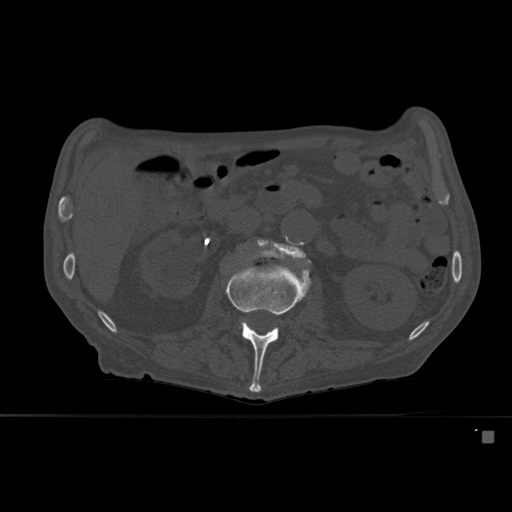
CT including the spine, one axial slice; bone window (W 1800 / L 400 HU); 1.5 mm slice thickness; 512 × 512 image matrix, field of view 373 × 373 mm. Patient: male, 78 years. From the clinical record (not read from this slice): primary cancer: prostate.
Structures marked on this image (semi-automatic segmentation, software-assisted and operator-edited):
- L2 vertebra: bounding box (x1, y1, x2, y2) in pixels: (226, 261, 311, 392)
- L3 vertebra: (241, 235, 310, 327)